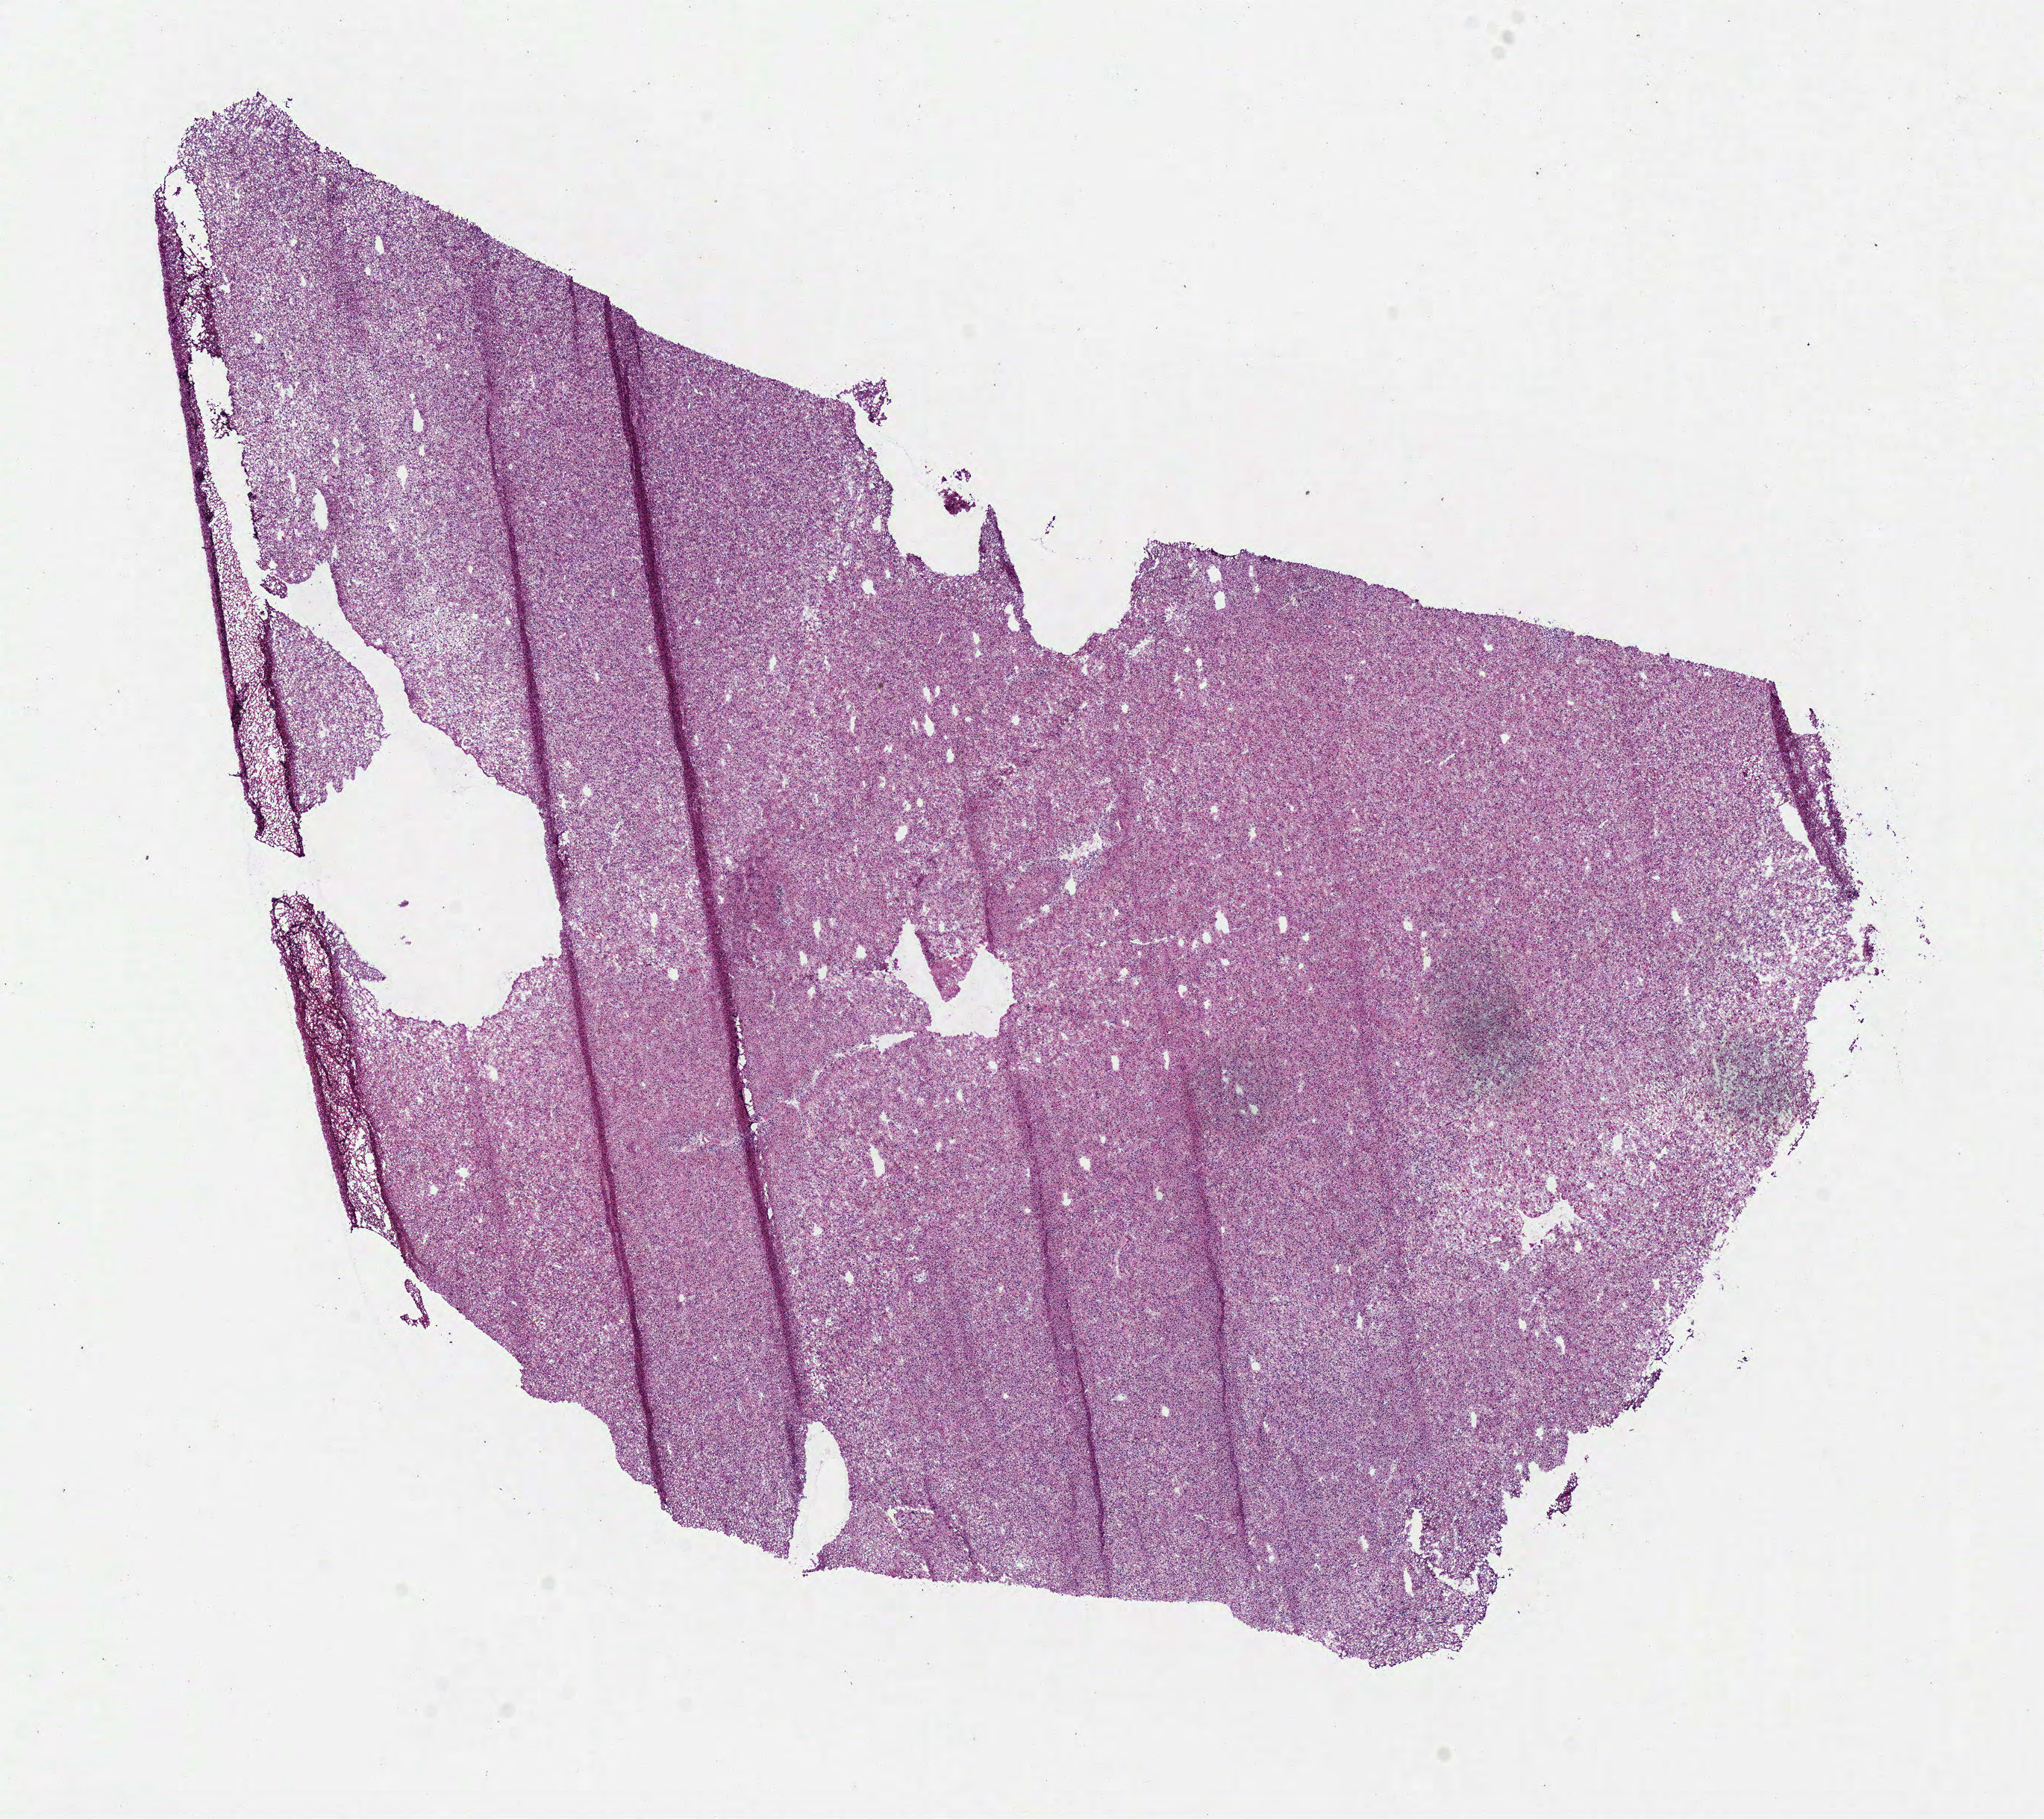
H&E-stained whole-slide image, whole scanned area (about 10.8 x 9.6 mm) shown as a low-resolution overview, frozen section from the bottom of the tissue portion, brain, primary tumour sample. Female patient; age at initial diagnosis 51 years. Histologic grade: G3 (poorly differentiated). Slide review estimates, as recorded: tumour cells 100%, tumour nuclei 80%, normal cells 0%, stromal cells 0%, necrosis 0%.
Diagnosis: Astrocytoma, anaplastic.